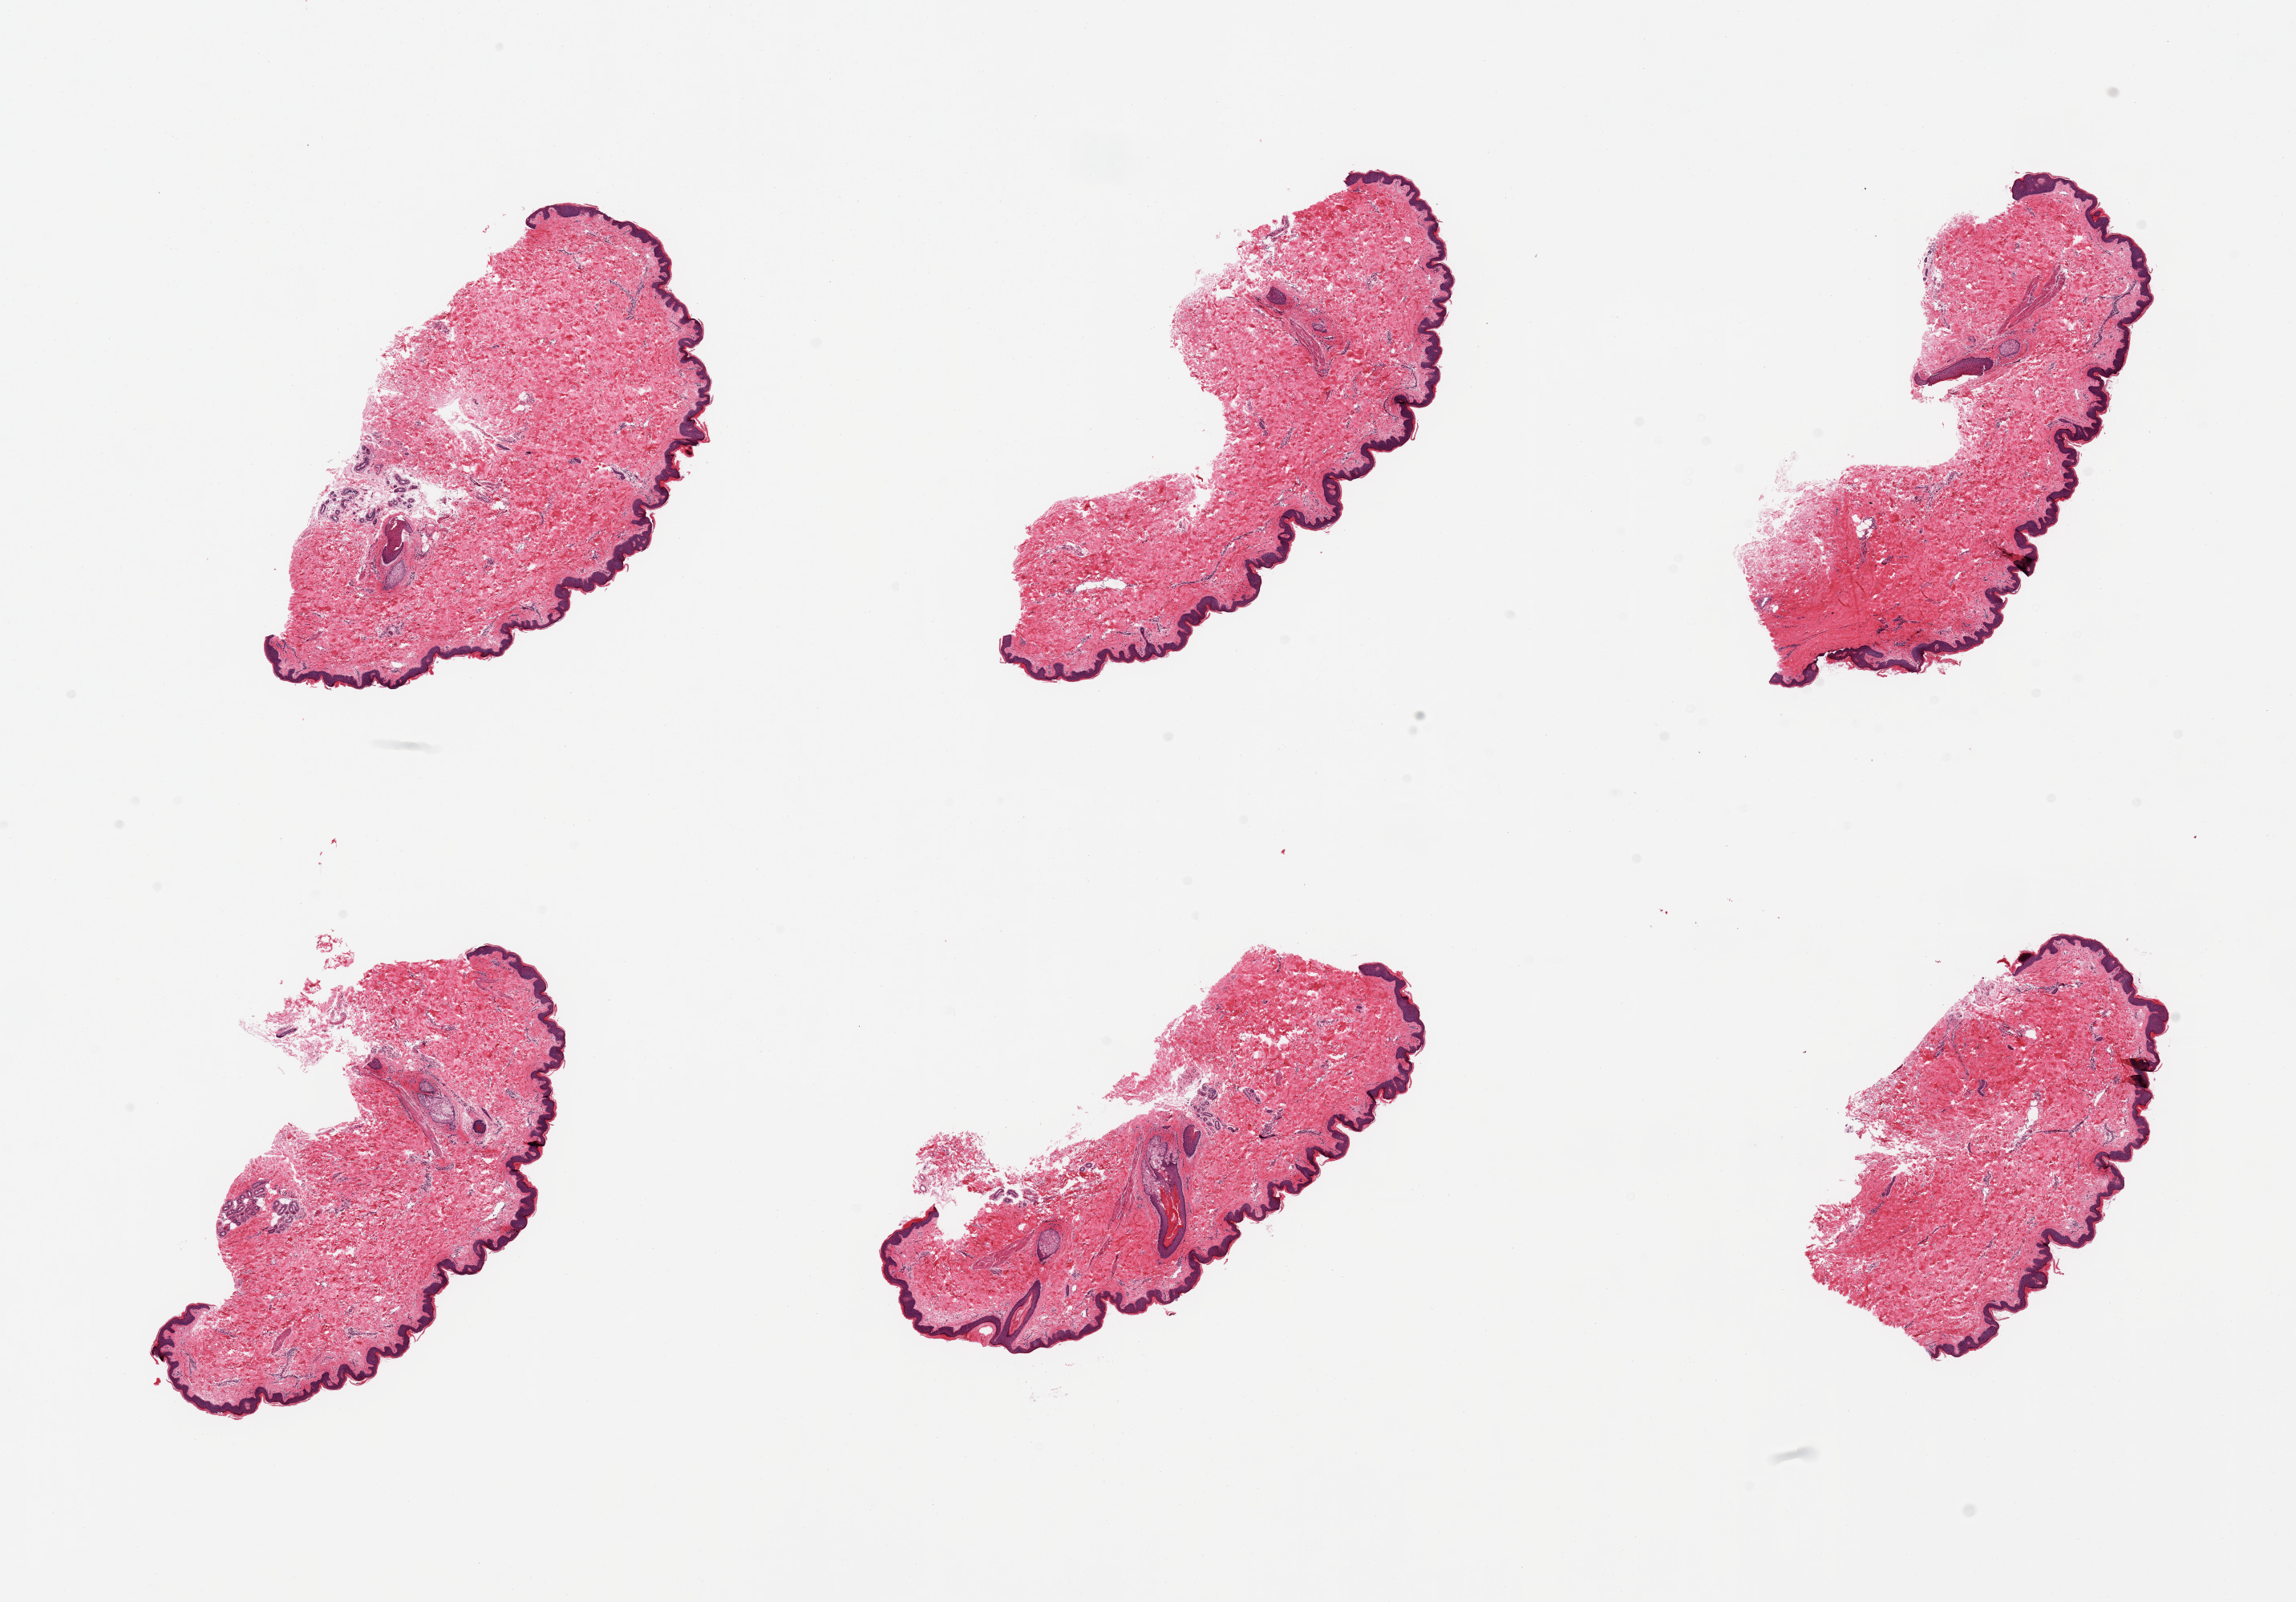
Digitized H&E-stained section — low-resolution overview of the scanned area, about 22.6 x 15.8 mm (slide scanned at 20x), PAXgene-fixed paraffin-embedded (PFPE) section, sampled site (target tissue): skin of suprapubic region, donor tissue sample.
Reviewer comment on this tissue sample: 6 pieces; well trimmed.